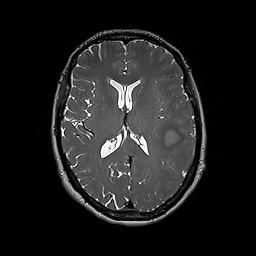
Brain MRI from a brain-tumour surgery series, one axial slice. Slice 94 of 192 in the series (ordered by position). 1 mm slice thickness. 256 × 256 image matrix. From the clinical record (not read from this slice): histopathology: Glioblastoma; WHO grade: 4; IDH mutation: no; tumour location: Left Frontal.
Annotated regions visible in this slice (manually delineated by an expert):
- tumour: bounding box <167,128,195,170> (left, top, right, bottom; pixels)